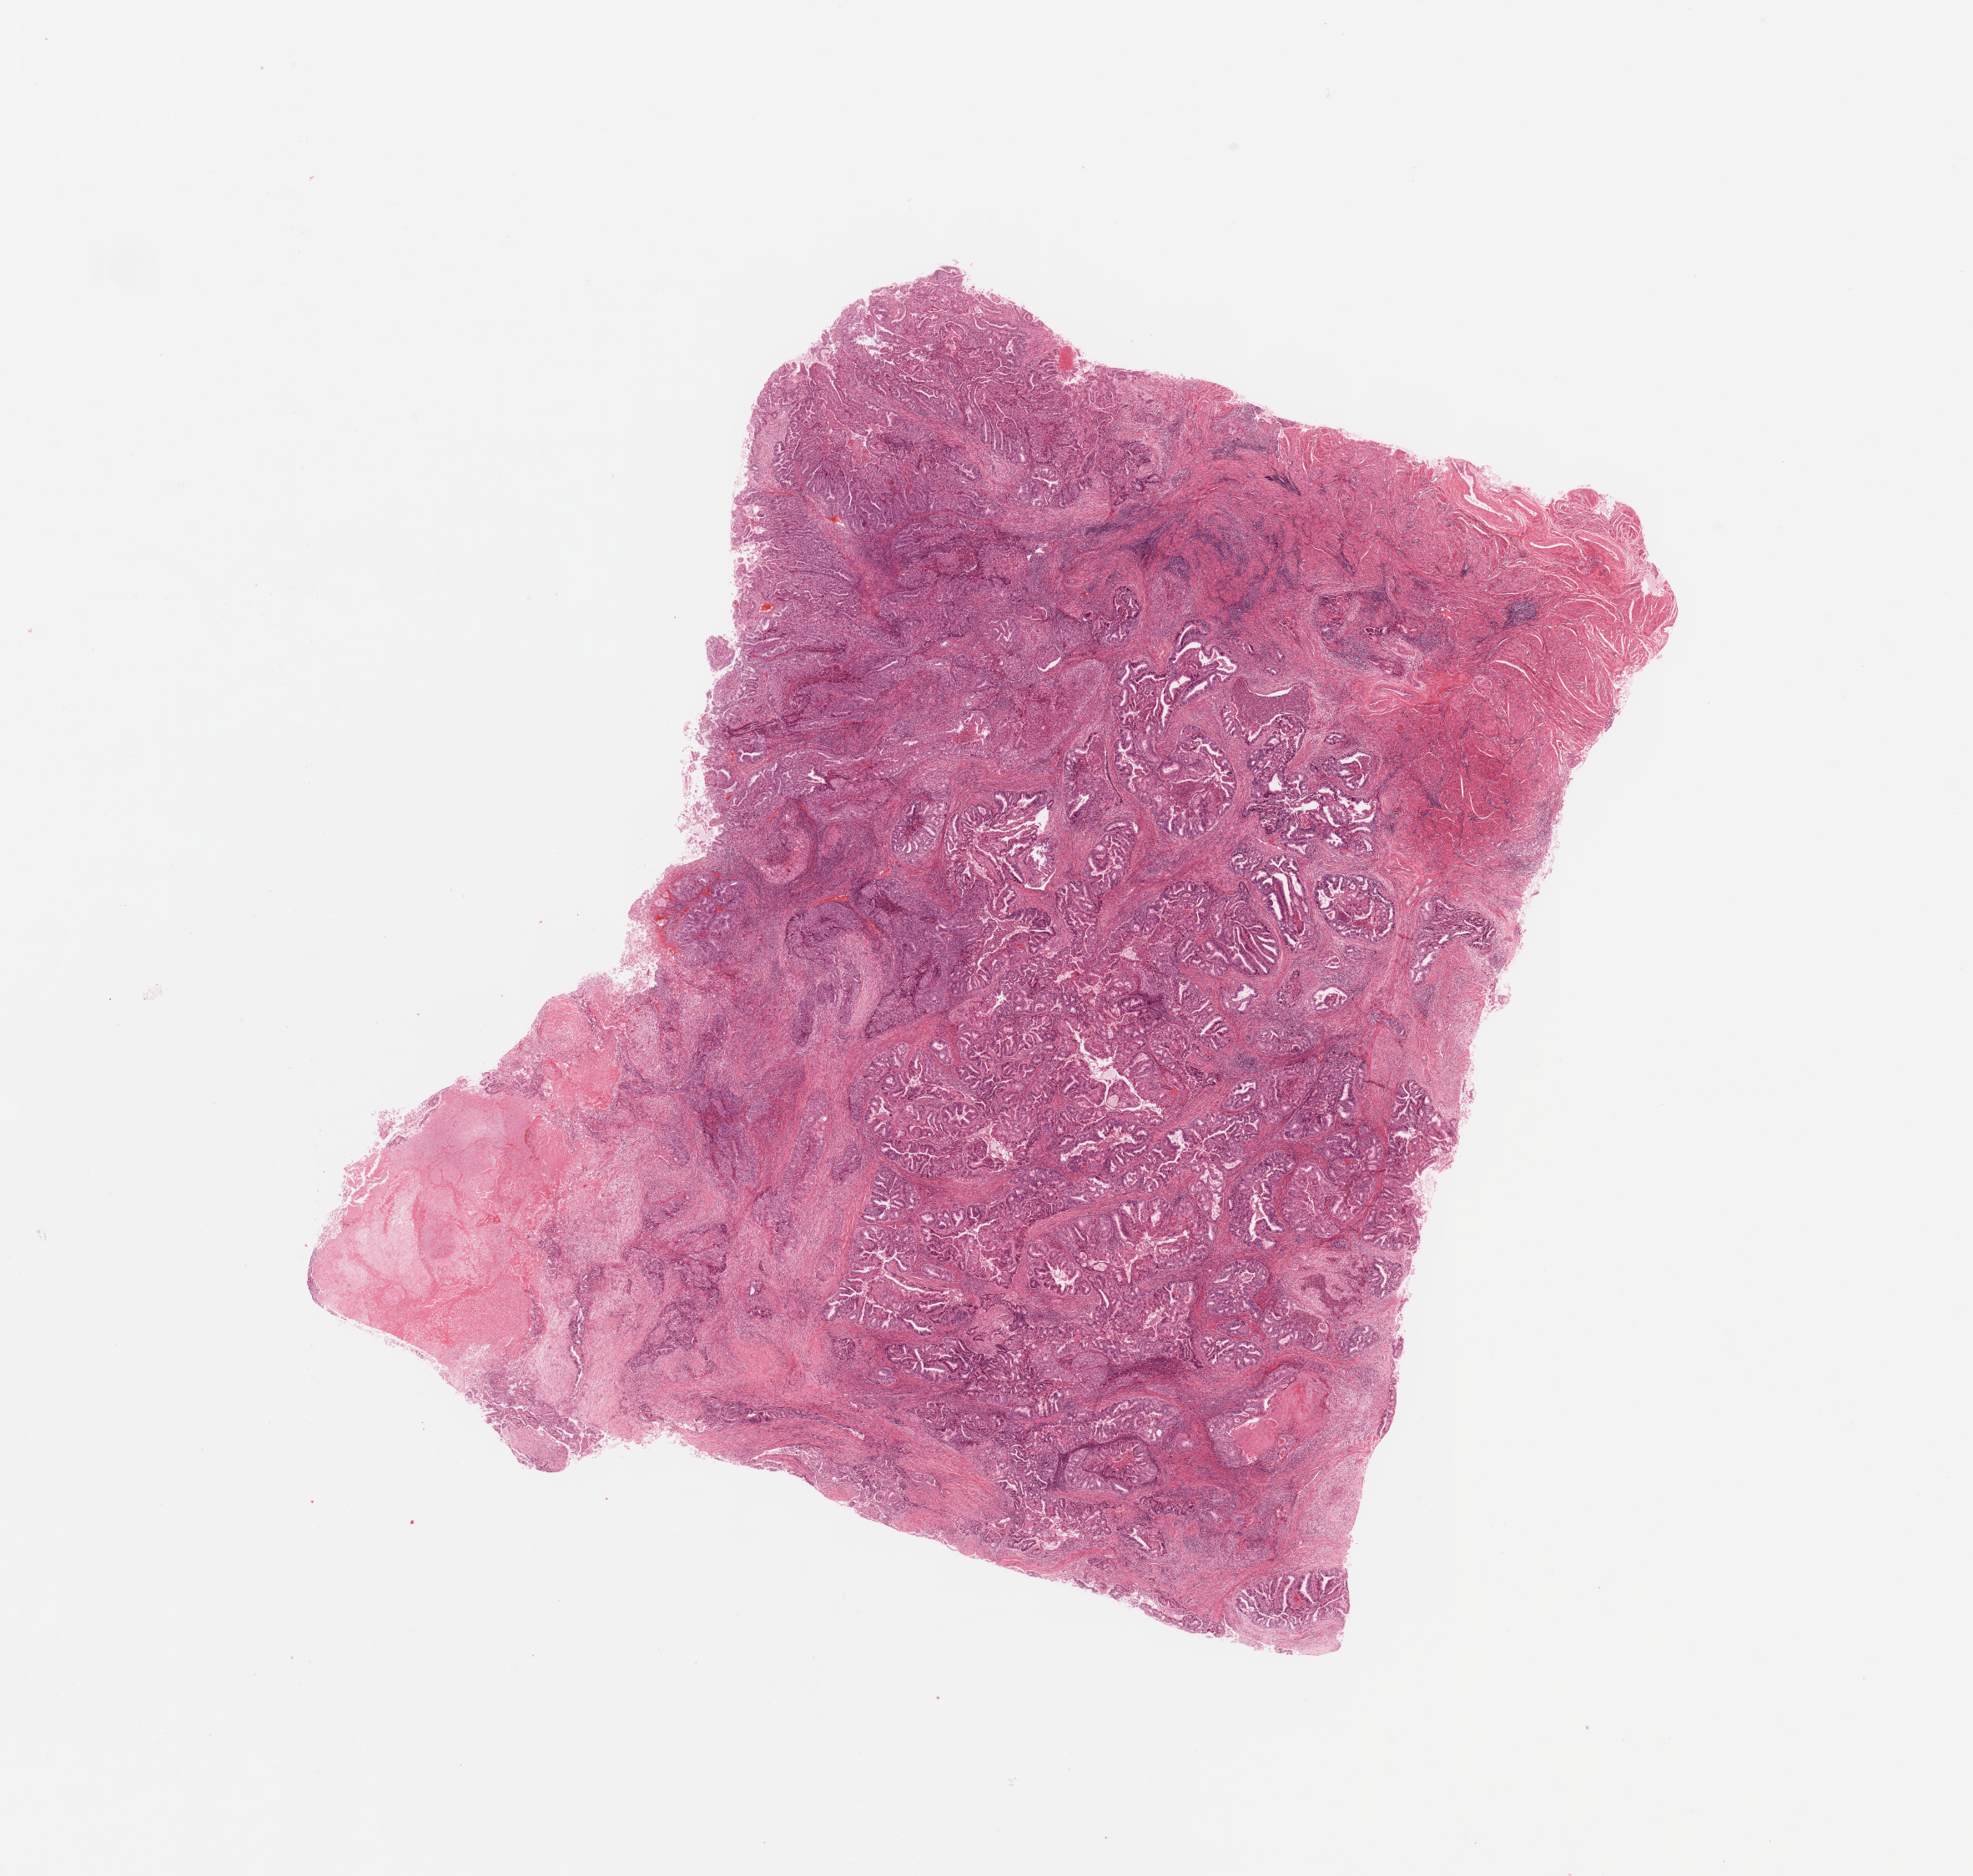
Hematoxylin and eosin (H&E) stained whole-slide image — shown as a low-resolution overview of the whole scanned area (about 18.7 x 17.8 mm); tumour tissue sample, uterus. Female, 60 y/o. Histologic grade: G3 (poorly differentiated).
AJCC pathologic stage: I. Histologic diagnosis: Endometrioid adenocarcinoma, NOS.